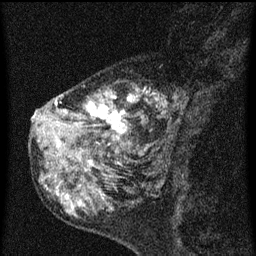
Breast MRI (dynamic contrast-enhanced), one sagittal slice. Slice 23 of 60 in the series (ordered by position). Dynamic contrast-enhanced series, image 2 of 3 at this slice position (ordered by acquisition). 1.5 T. TE 4.2 ms, TR 8 ms. 2 mm slice thickness. 256 × 256 image matrix, field of view 180 × 180 mm. Female patient, age 55 years.
Annotated regions visible in this slice (semi-automatic segmentation, software-assisted and operator-edited):
- analysis volume of interest (the breast-tissue region the enhancement analysis was run in; not a lesion): bounding box <42,74,183,155> (left, top, right, bottom; pixels)
- tumour enhancement mask (voxels above the 70 % enhancement threshold inside the analysis volume of interest): <56,90,168,151>